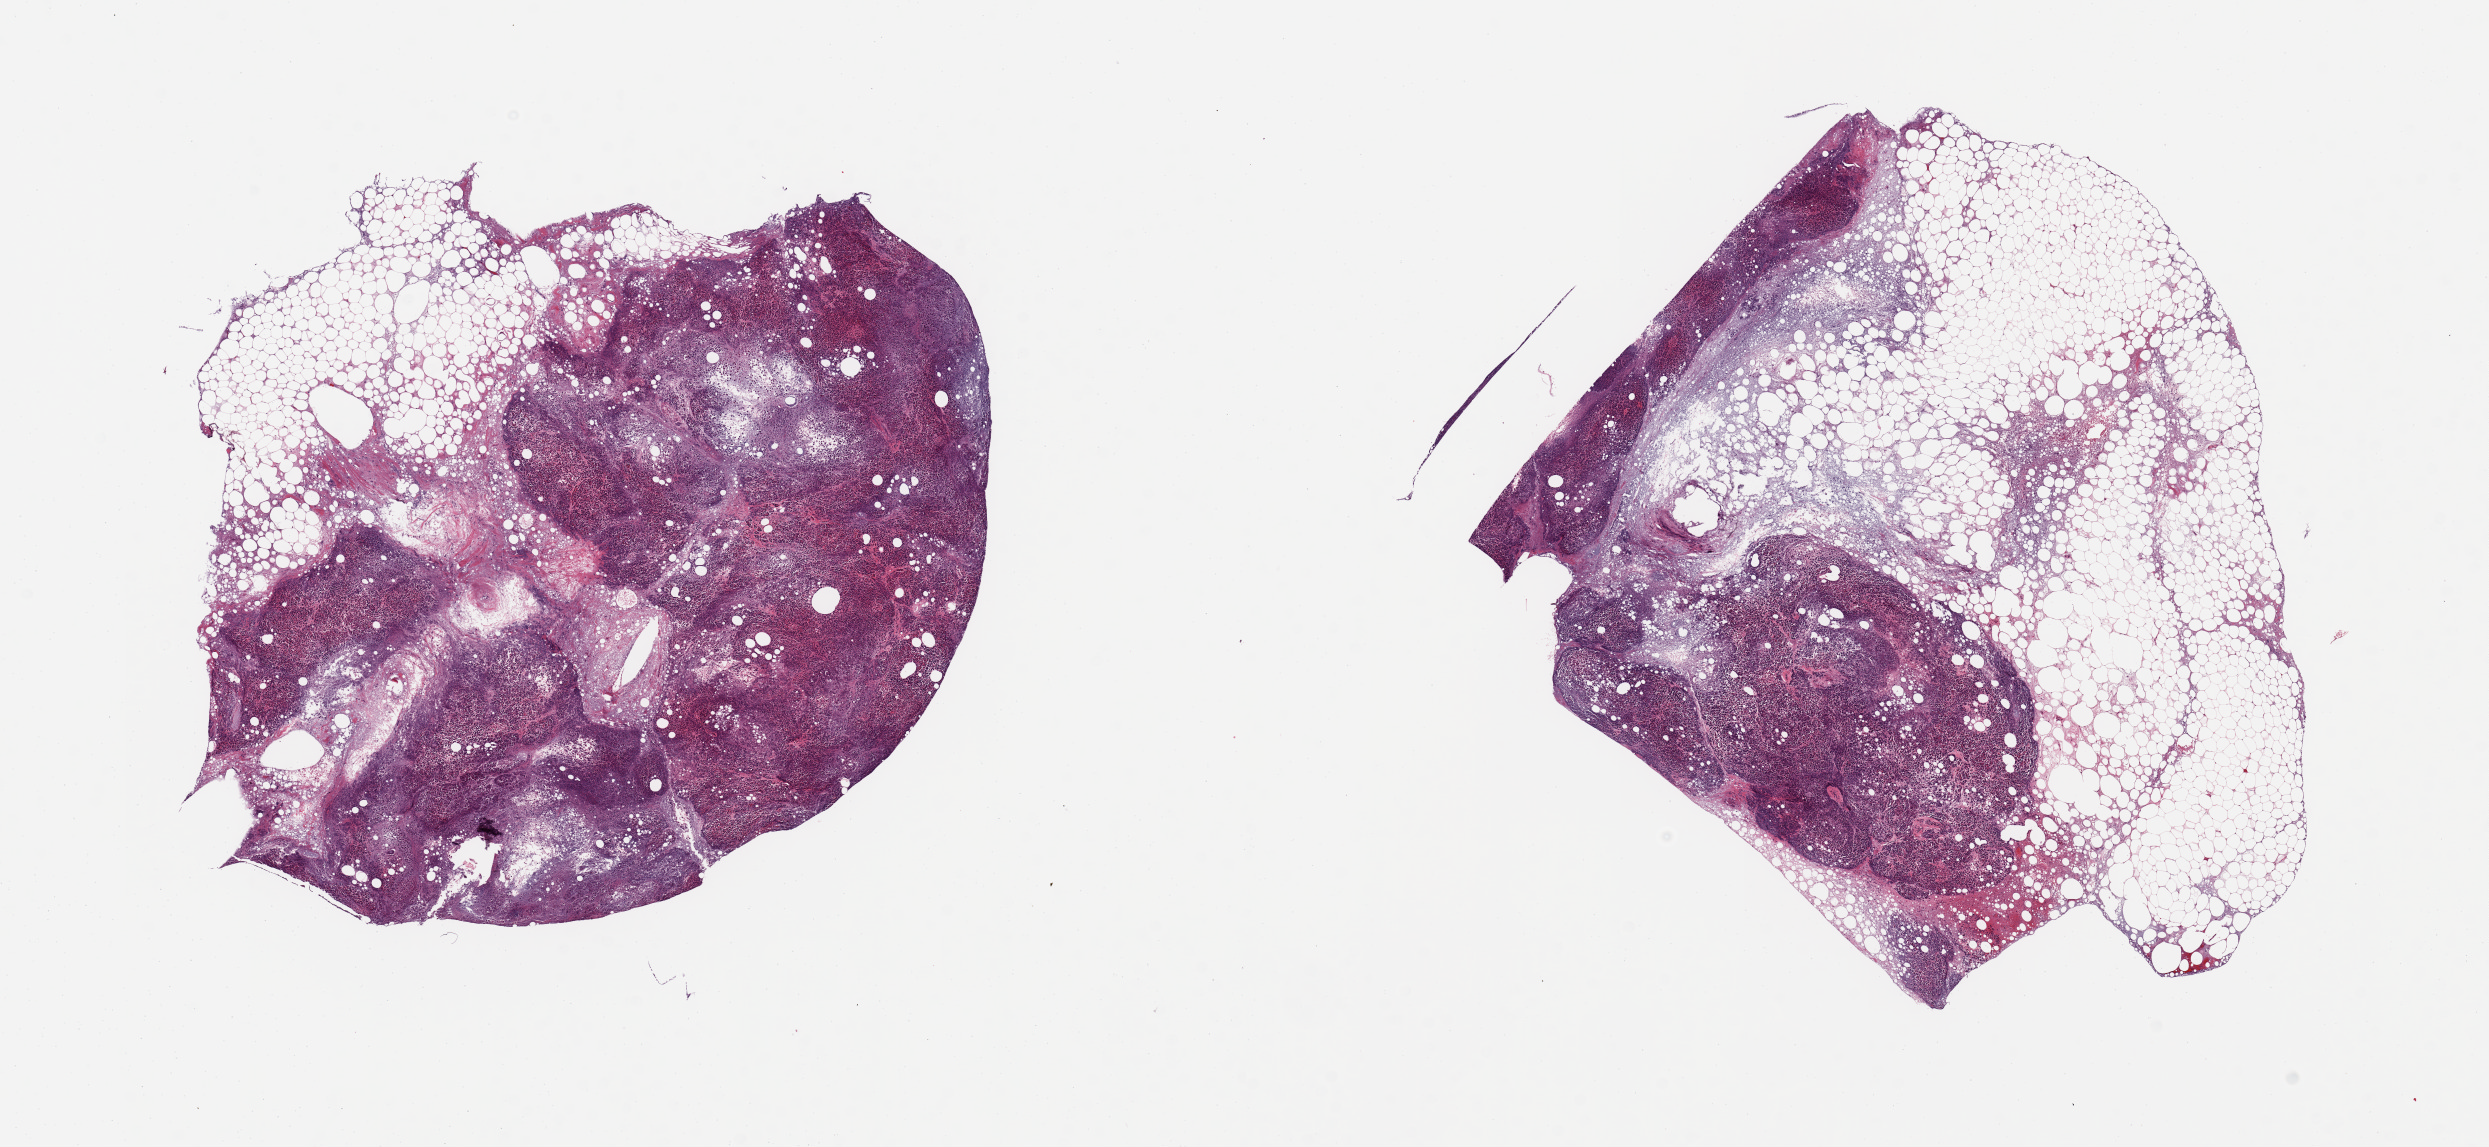
Hematoxylin and eosin (H&E) whole-slide image — shown as a low-resolution overview of the whole scanned area (about 19.7 x 9.1 mm). Donor sex: male.
• specimen: PAXgene-fixed, paraffin-embedded tissue; section of pancreas (target tissue); tissue donor sample